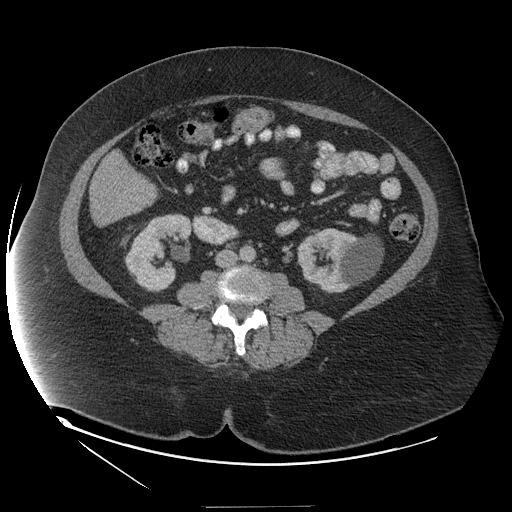
Contrast-enhanced abdominal CT (liver protocol), one axial slice. Slice 29 of 127 in the series (ordered by position). Reconstruction kernel STANDARD. Soft-tissue window (W 400 / L 40 HU). 2.5 mm slice thickness. 512 × 512 image matrix, field of view 480 × 480 mm. From the clinical record (not read from this slice): diagnosis: hepatocellular carcinoma (patient treated with transarterial chemoembolisation; whether this scan precedes or follows treatment is not stated here); TNM stage (as recorded): Stage-II; Child-Pugh class: A; tumour nodularity: multinodular.
Structures marked on this image (semi-automatic segmentation, software-assisted and operator-edited):
- liver parenchyma outside the tumour (the mass and vessels are separate outlines, so this box may not span the whole liver): box from (x=92, y=202) to (x=122, y=224) px